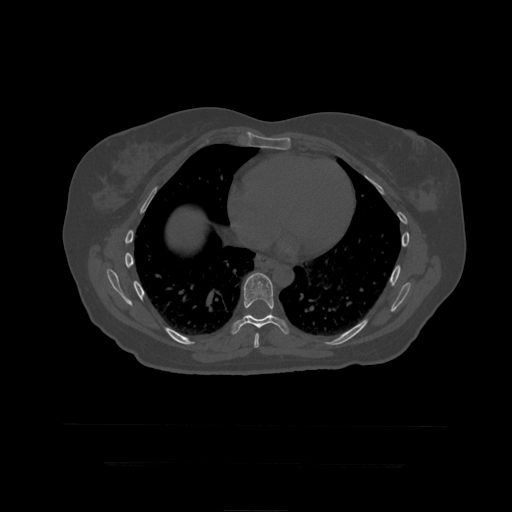
CT including the spine, one axial slice; position 263 of 399 along the scan axis; reconstruction kernel STANDARD; bone window (W 1800 / L 400 HU); 1.25 mm slice thickness; 512 × 512 image matrix. Patient age 41 years. Case-level facts recorded for this patient, not image findings: primary cancer: breast.
Annotated regions visible in this slice (semi-automatically segmented with operator editing):
- T8 vertebra: bounding box [x1, y1, x2, y2] px = [254, 333, 259, 349]
- T9 vertebra: [232, 273, 289, 335]